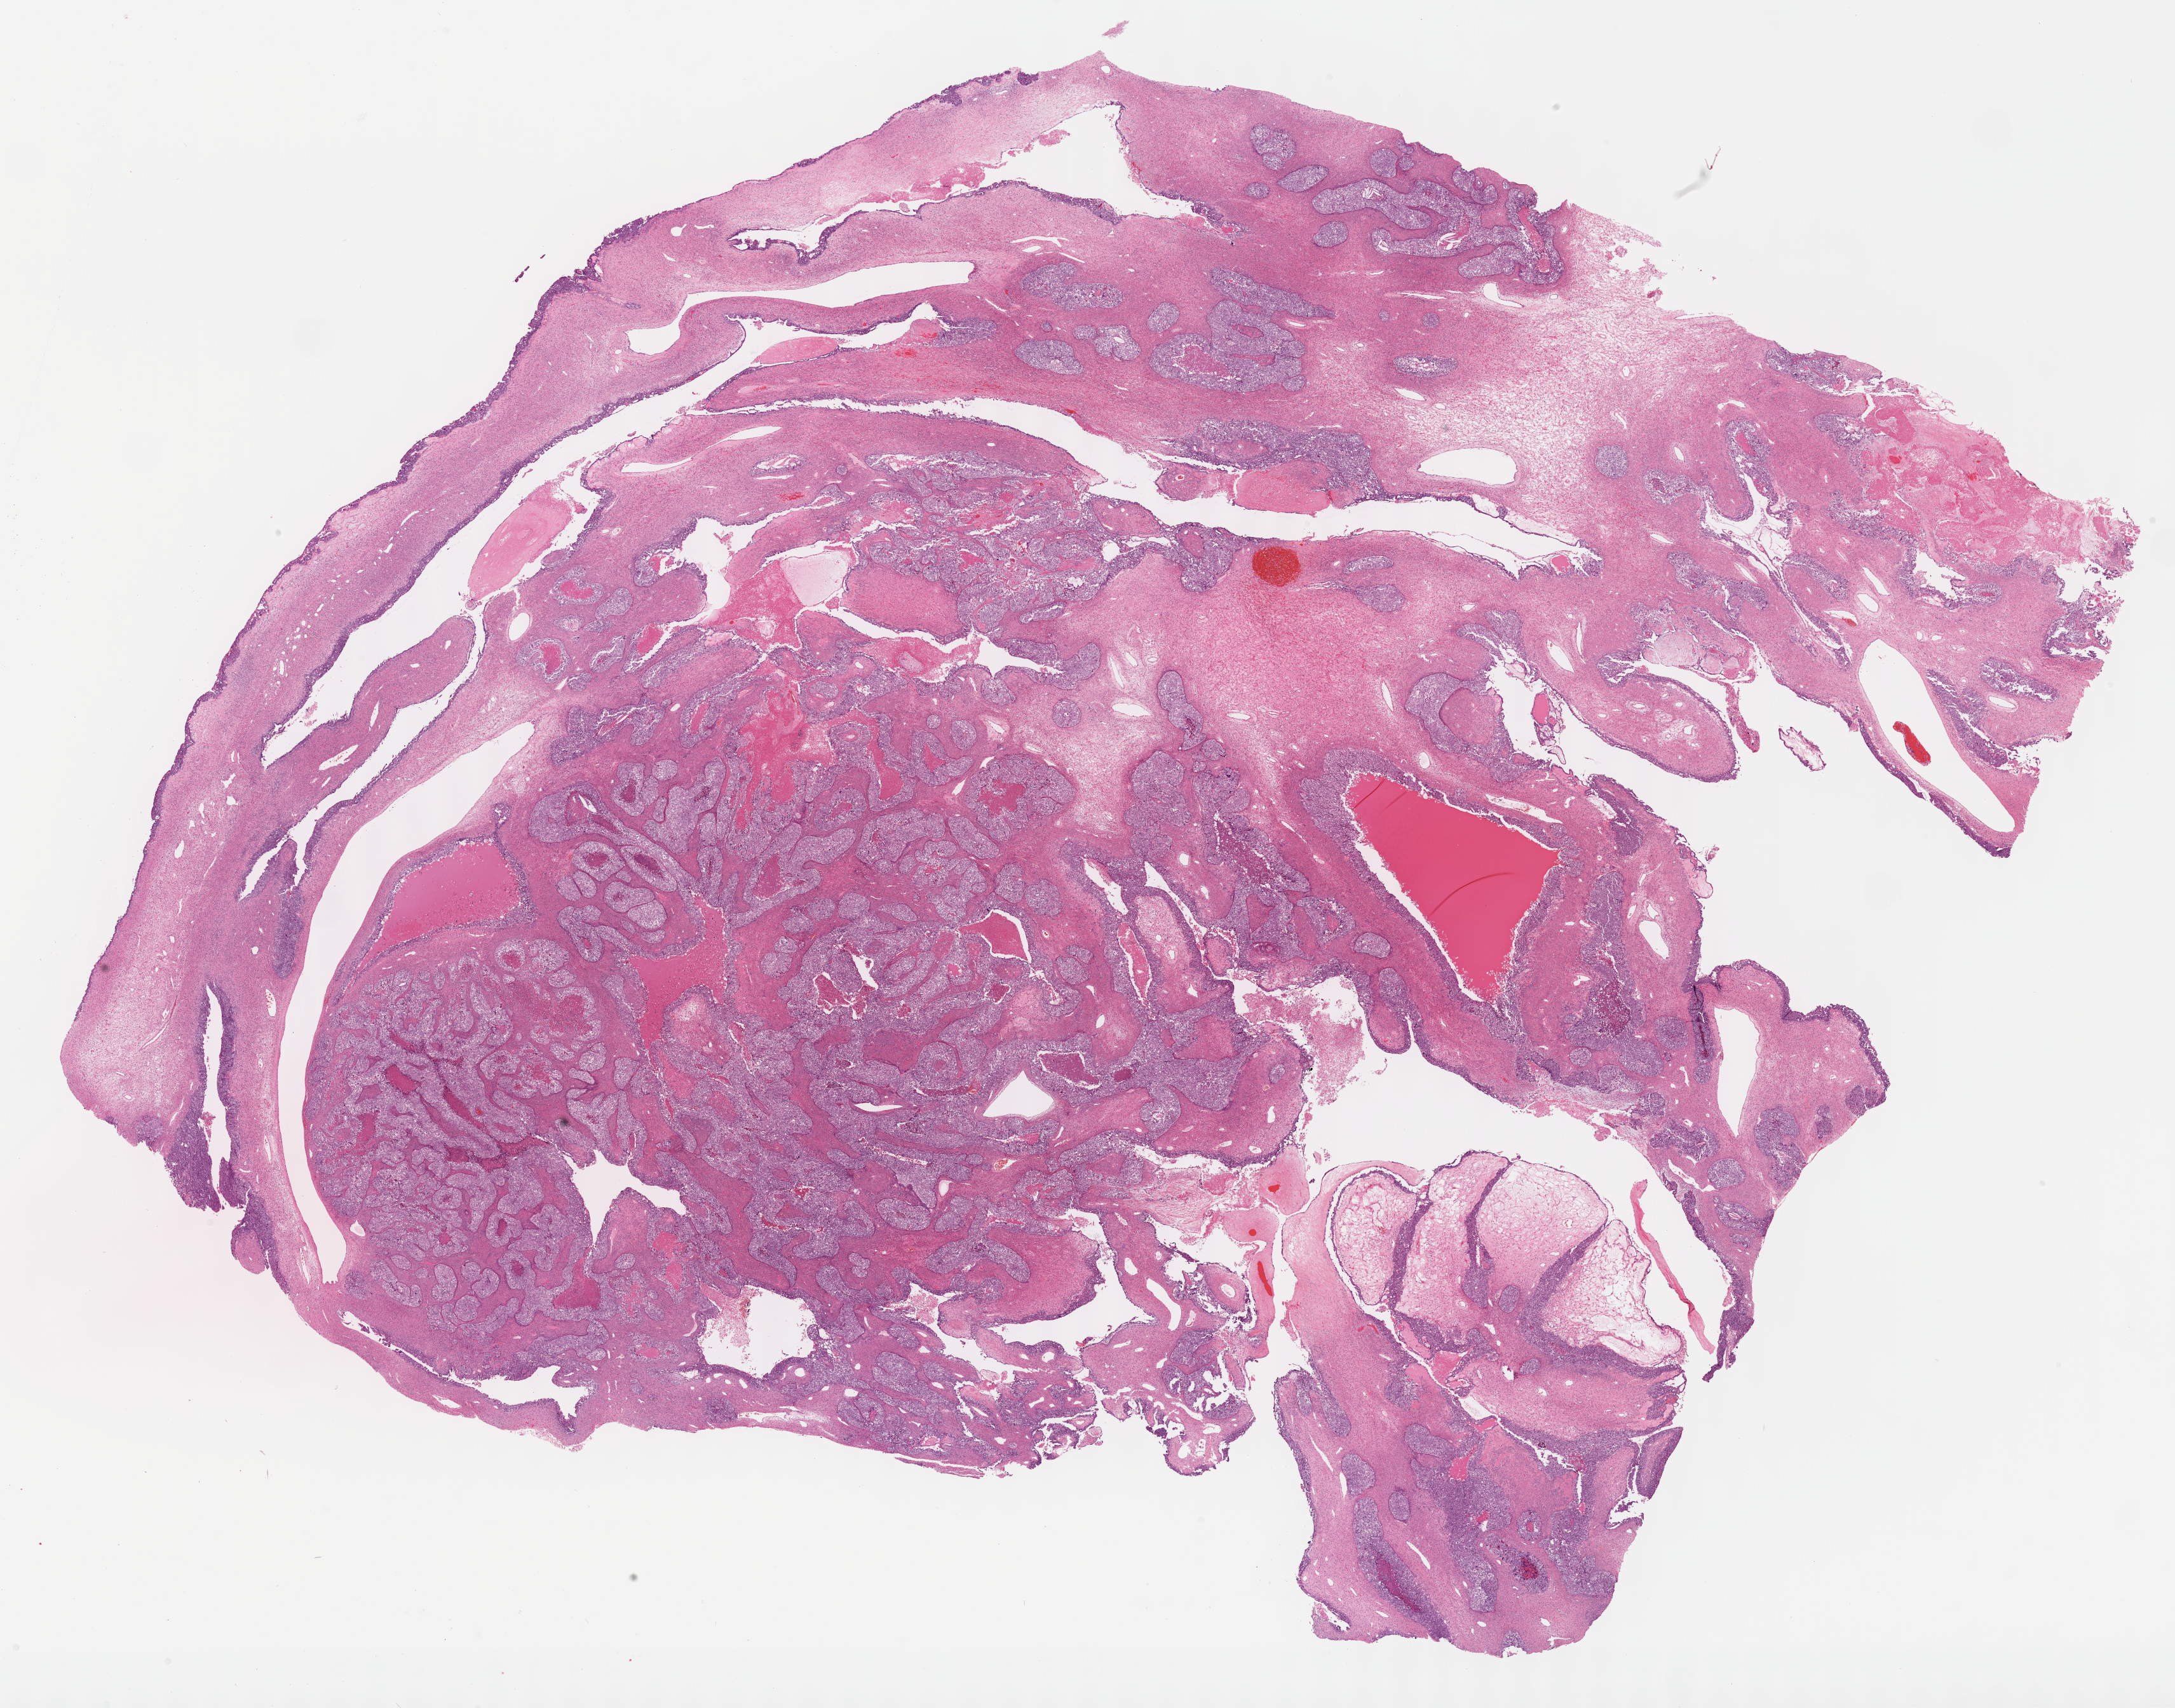
Digitized H&E tissue section (whole slide), shown as a low-resolution overview of the whole scanned area (about 27.7 x 21.7 mm, from a 40x scan). Formalin-fixed paraffin-embedded (FFPE) diagnostic section. Sample: primary tumour, ovary. Female patient; age at initial diagnosis 63 years.
Pathologic diagnosis: Serous cystadenocarcinoma, NOS.